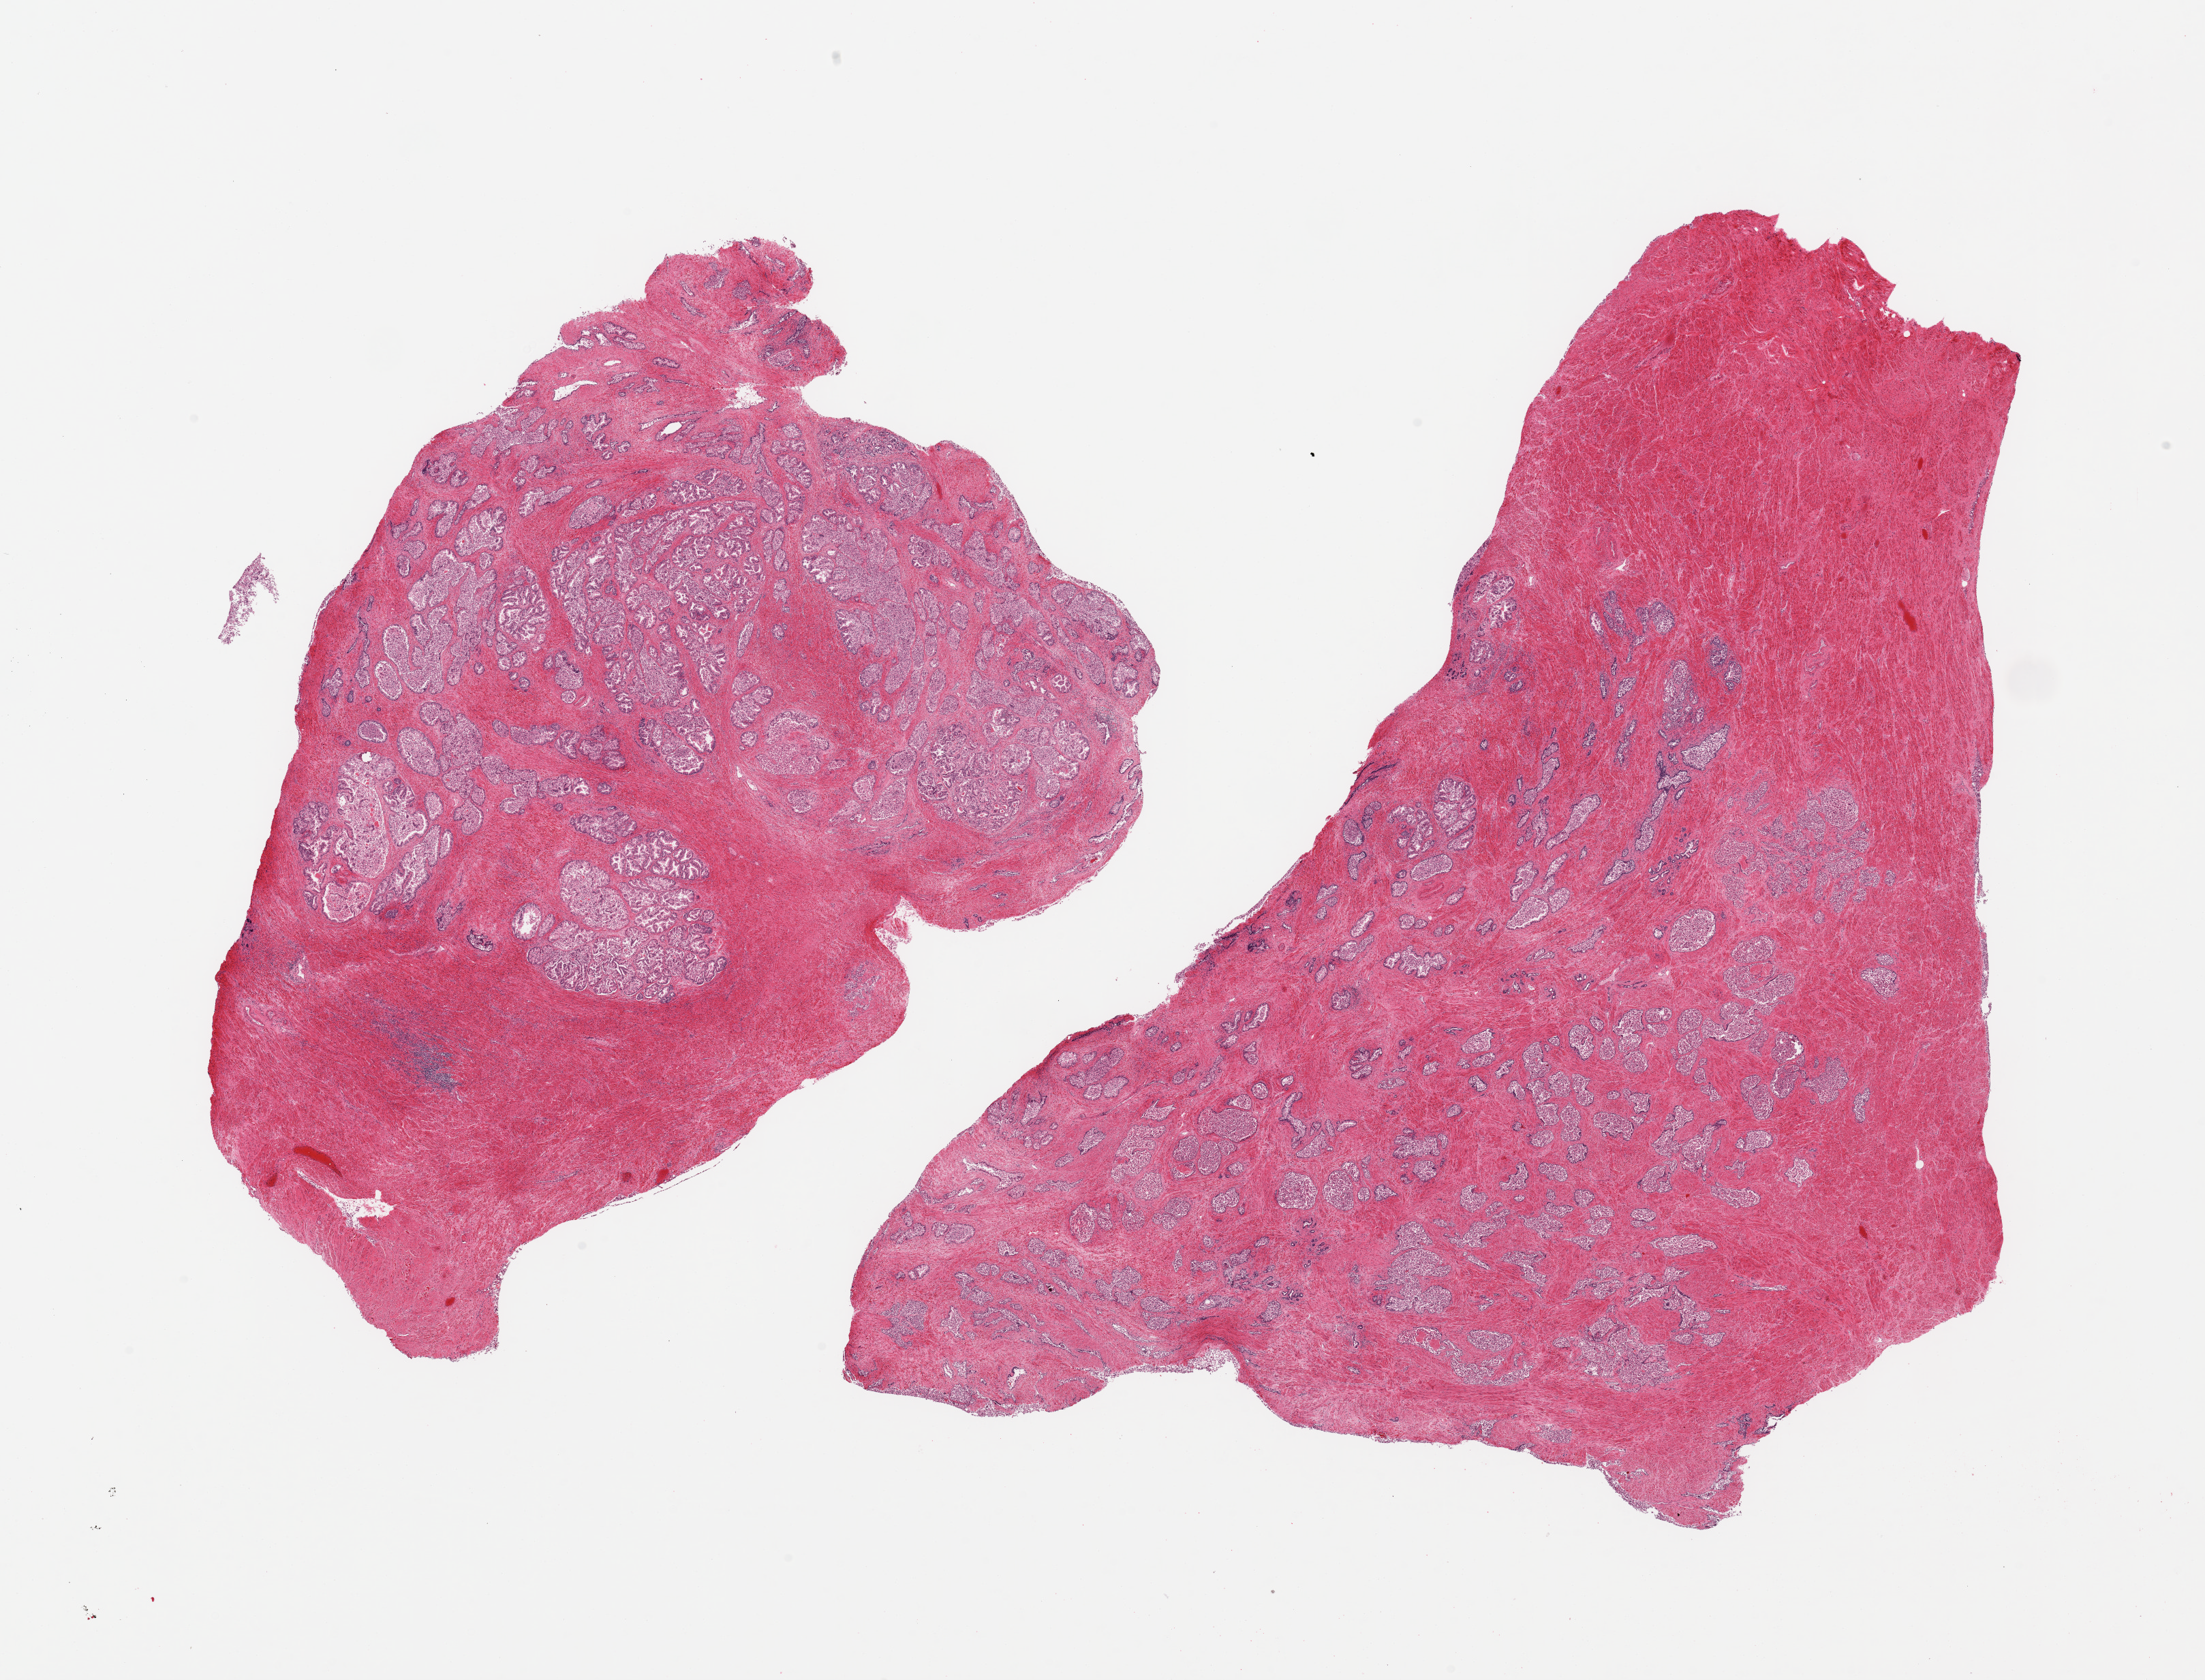
H&E whole-slide image, whole scanned area (about 25.6 x 19.5 mm, from a 20x scan) shown as a low-resolution overview. PAXgene-fixed paraffin-embedded (PFPE) section. Sampled site (target tissue): prostate. Tissue donor sample. Donor sex: male.
Pathologist's review note for this sample: 2 pieces, glandular elements with hyperplastic pattern, variably but generally moderately autolyzed.